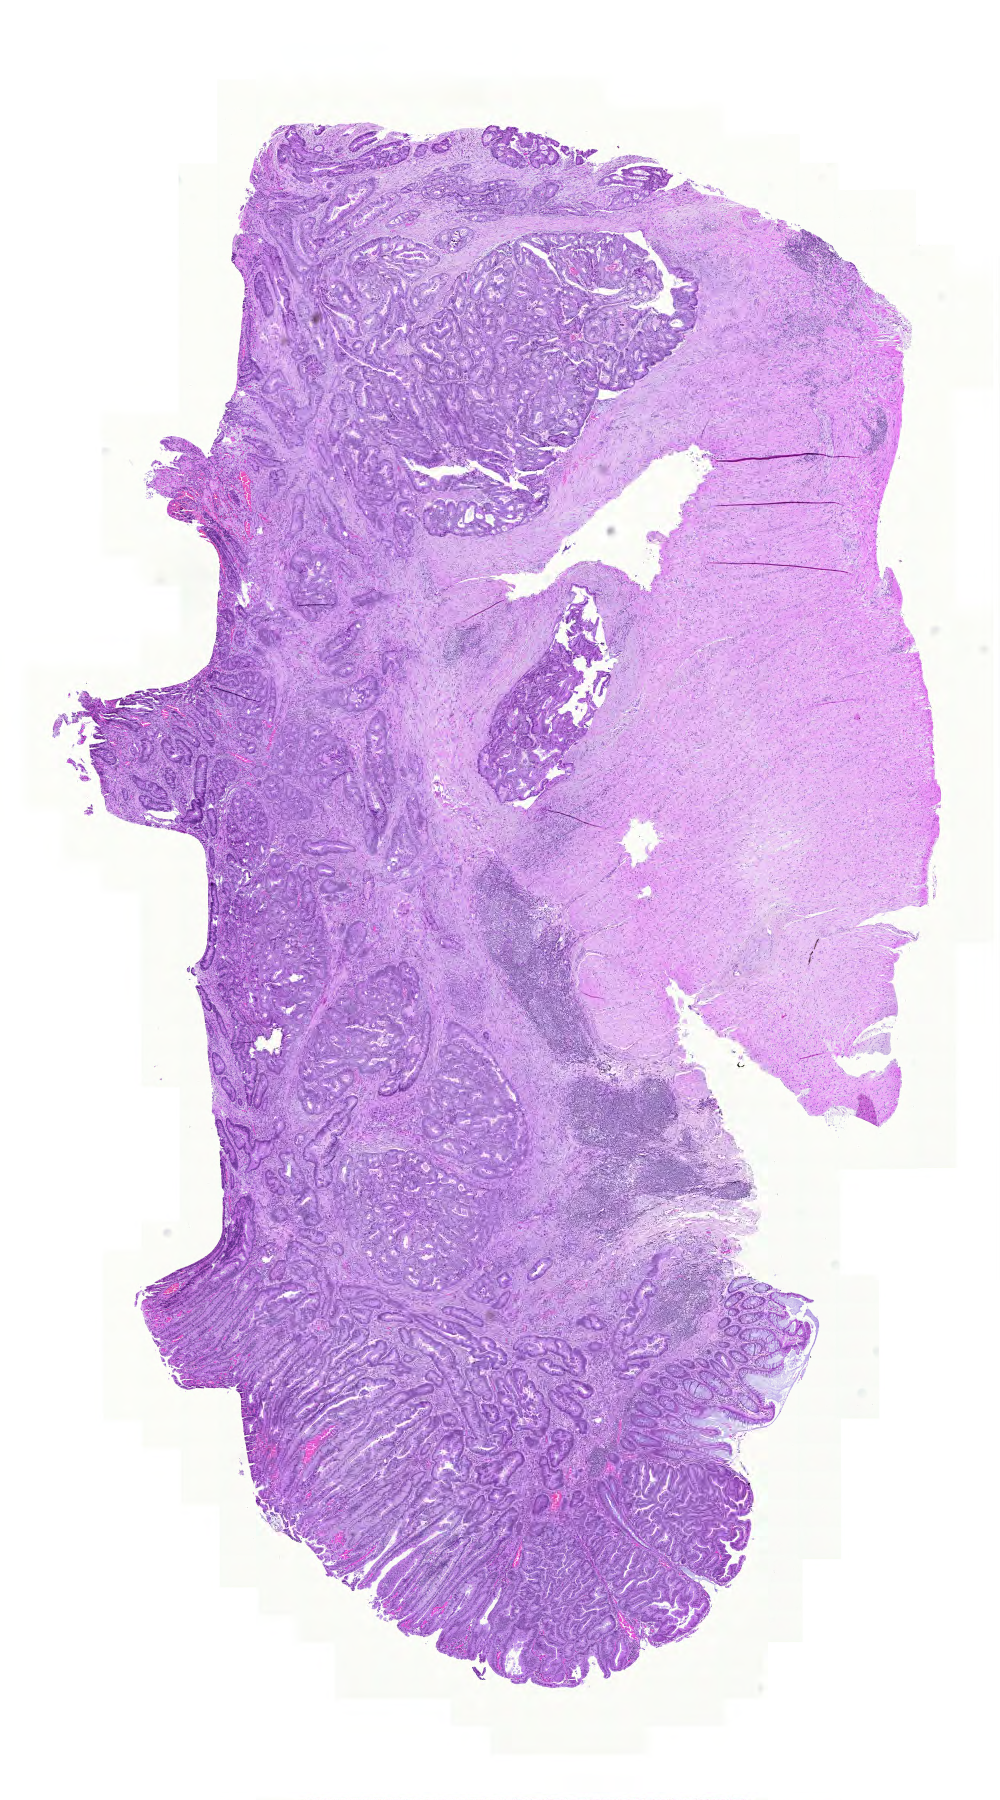
Digitized Hematoxylin and eosin (H&E) stained tissue section (whole slide), whole scanned area (about 7.4 x 13.4 mm) shown as a low-resolution overview; FFPE section; sample: primary tumour, rectum. Female, age 59 years at initial diagnosis.
Pathologic diagnosis: Adenocarcinoma, NOS. AJCC pathologic stage: II (5th edition). Lymph nodes positive (case pathology): 0 of 12 examined.